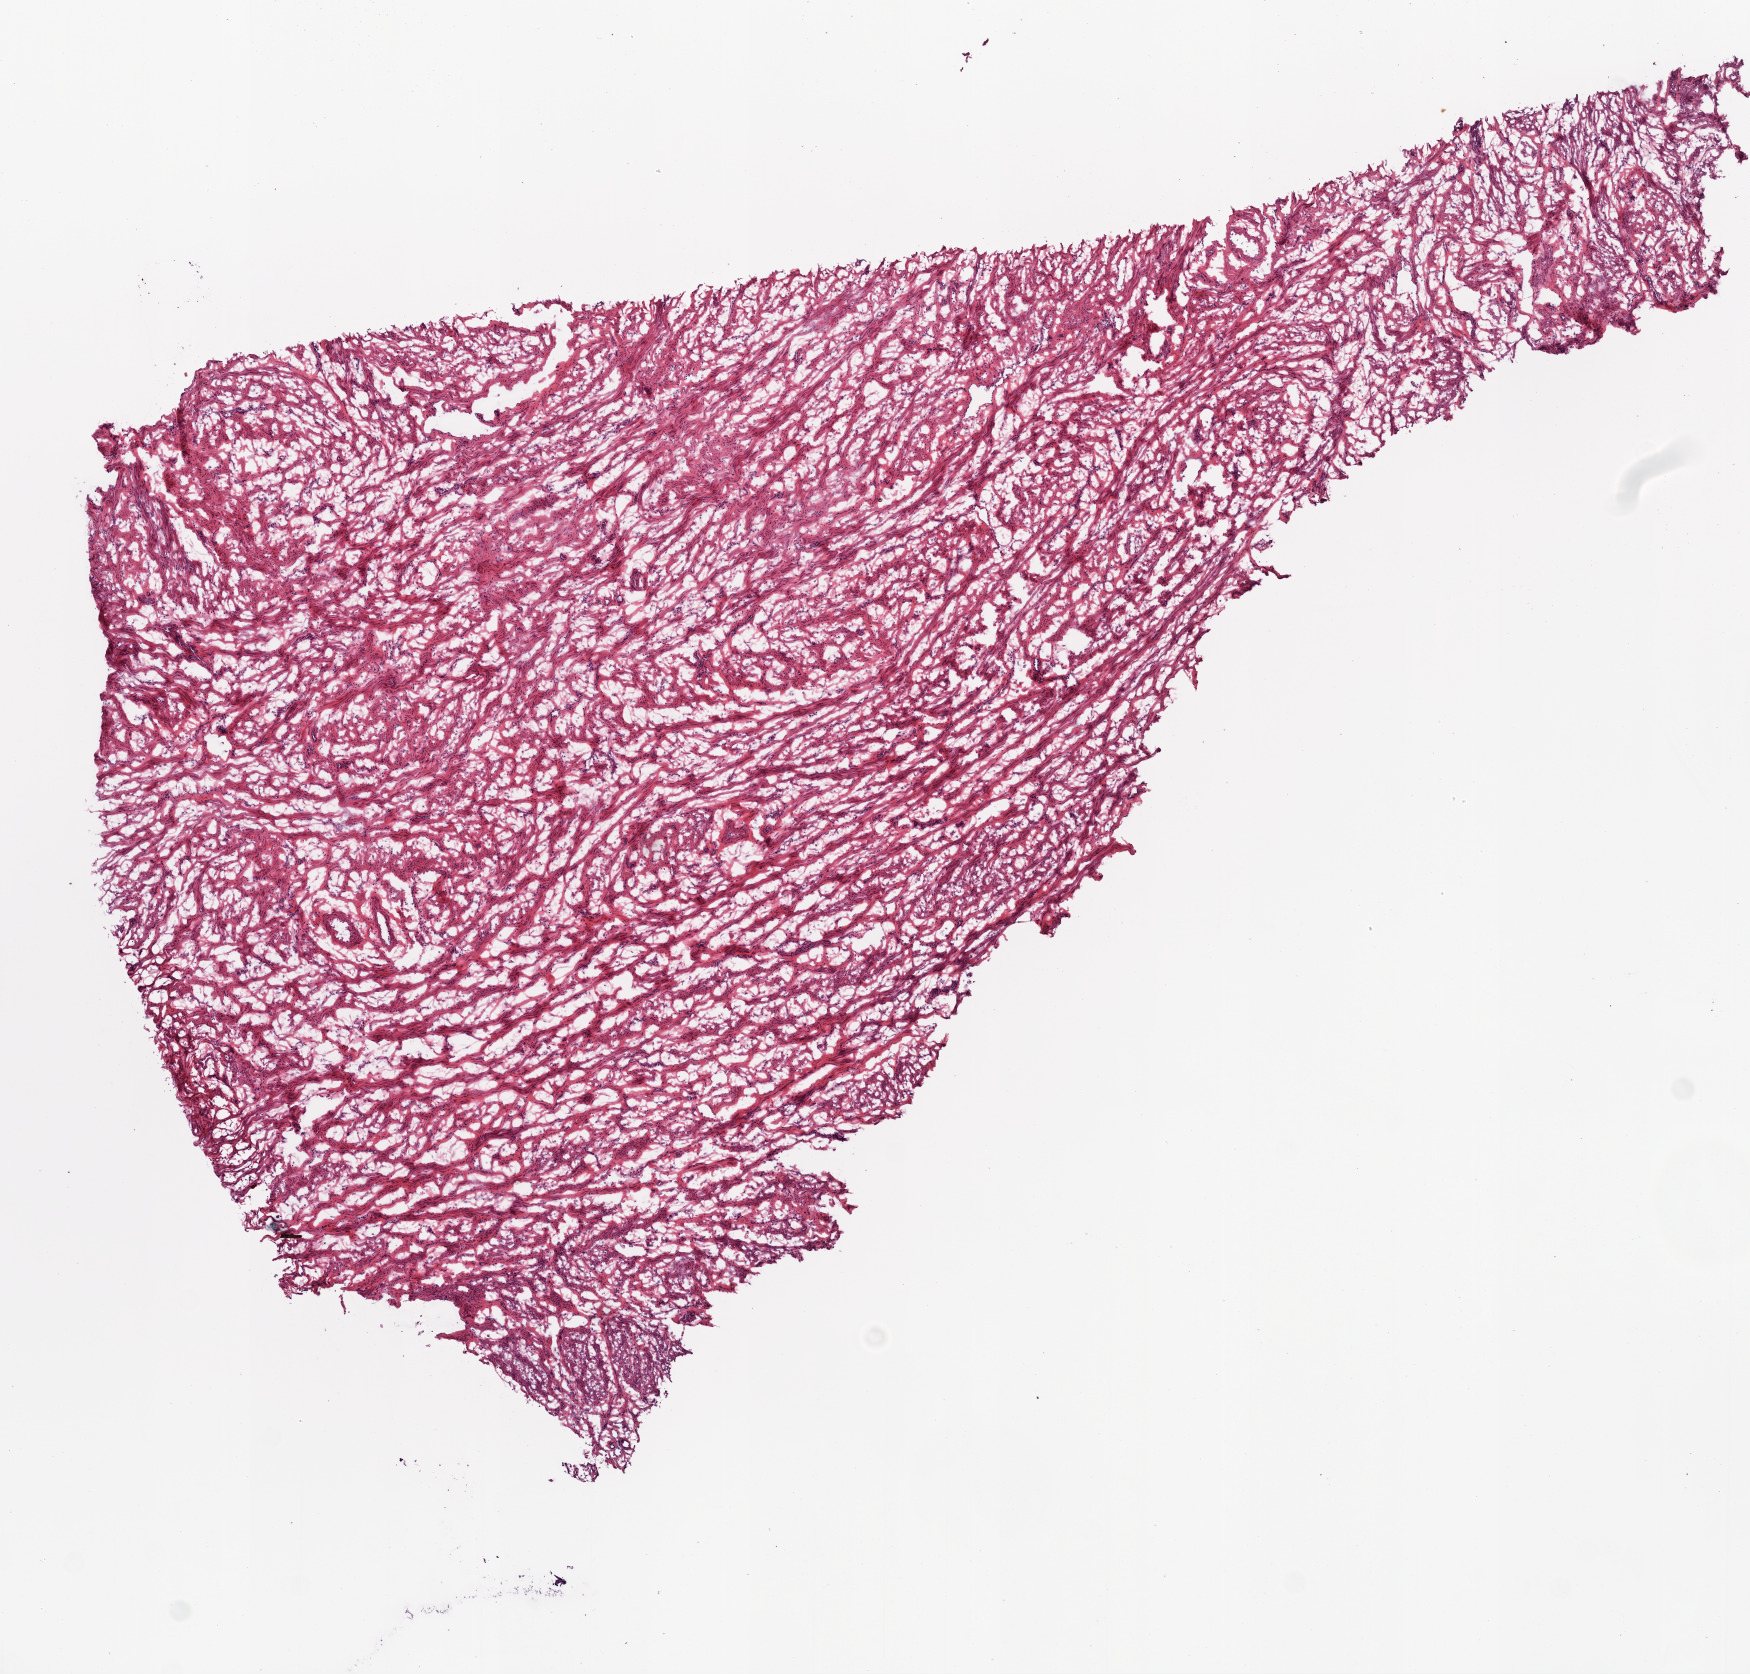
Whole-slide histology image, Hematoxylin and eosin (H&E) stained — whole scanned area (about 7.0 x 6.7 mm, acquisition: 20x scan) shown as a low-resolution overview. Frozen section. Sample: solid tissue normal (non-tumour tissue), ovary. Female, age 47 years at initial diagnosis.
This section: solid tissue normal sample (biorepository sample class). Patient diagnosis: Serous cystadenocarcinoma, NOS.